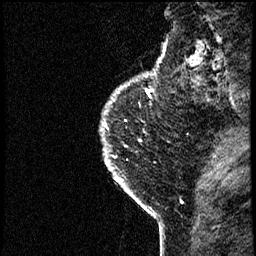
Breast MRI (dynamic contrast-enhanced), one sagittal slice. Position 57 of 60 along the scan axis. Dynamic contrast-enhanced study with each time point stored as its own series, time point 2 of 4 at this slice position (early post-contrast, ordered by acquisition time). 1.5 T. TE 4.2 ms, TR 17.6 ms. 2 mm slice thickness. 256 × 256 image matrix. Patient: female, 40 years. From the clinical record (not read from this slice): setting: breast cancer imaged before/during neoadjuvant chemotherapy; receptor status: HER2-positive.
Structures marked on this image (semi-automatically segmented with operator editing):
- analysis volume of interest (the breast-tissue region the enhancement analysis was run in; not a lesion): bounding box (x1, y1, x2, y2) in pixels: (94, 55, 185, 206)
- tumour enhancement mask (voxels above the 100 % enhancement threshold inside the analysis volume of interest): (106, 55, 163, 184)